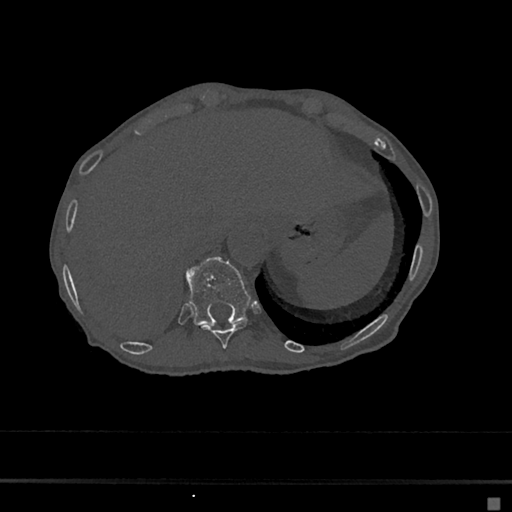
CT including the spine, one axial slice; position 195 of 797 along the scan axis; reconstruction kernel Br40s/3; 120 kVp; bone window (W 1800 / L 400 HU); 512 × 512 image matrix, field of view 360 × 360 mm. Female patient, age 68 years. From the clinical record (not read from this slice): primary cancer: renal.
Annotated regions visible in this slice (semi-automatically segmented with operator editing):
- T10 vertebra: bounding box [x1, y1, x2, y2] px = [201, 321, 248, 349]
- T11 vertebra: [187, 258, 251, 325]